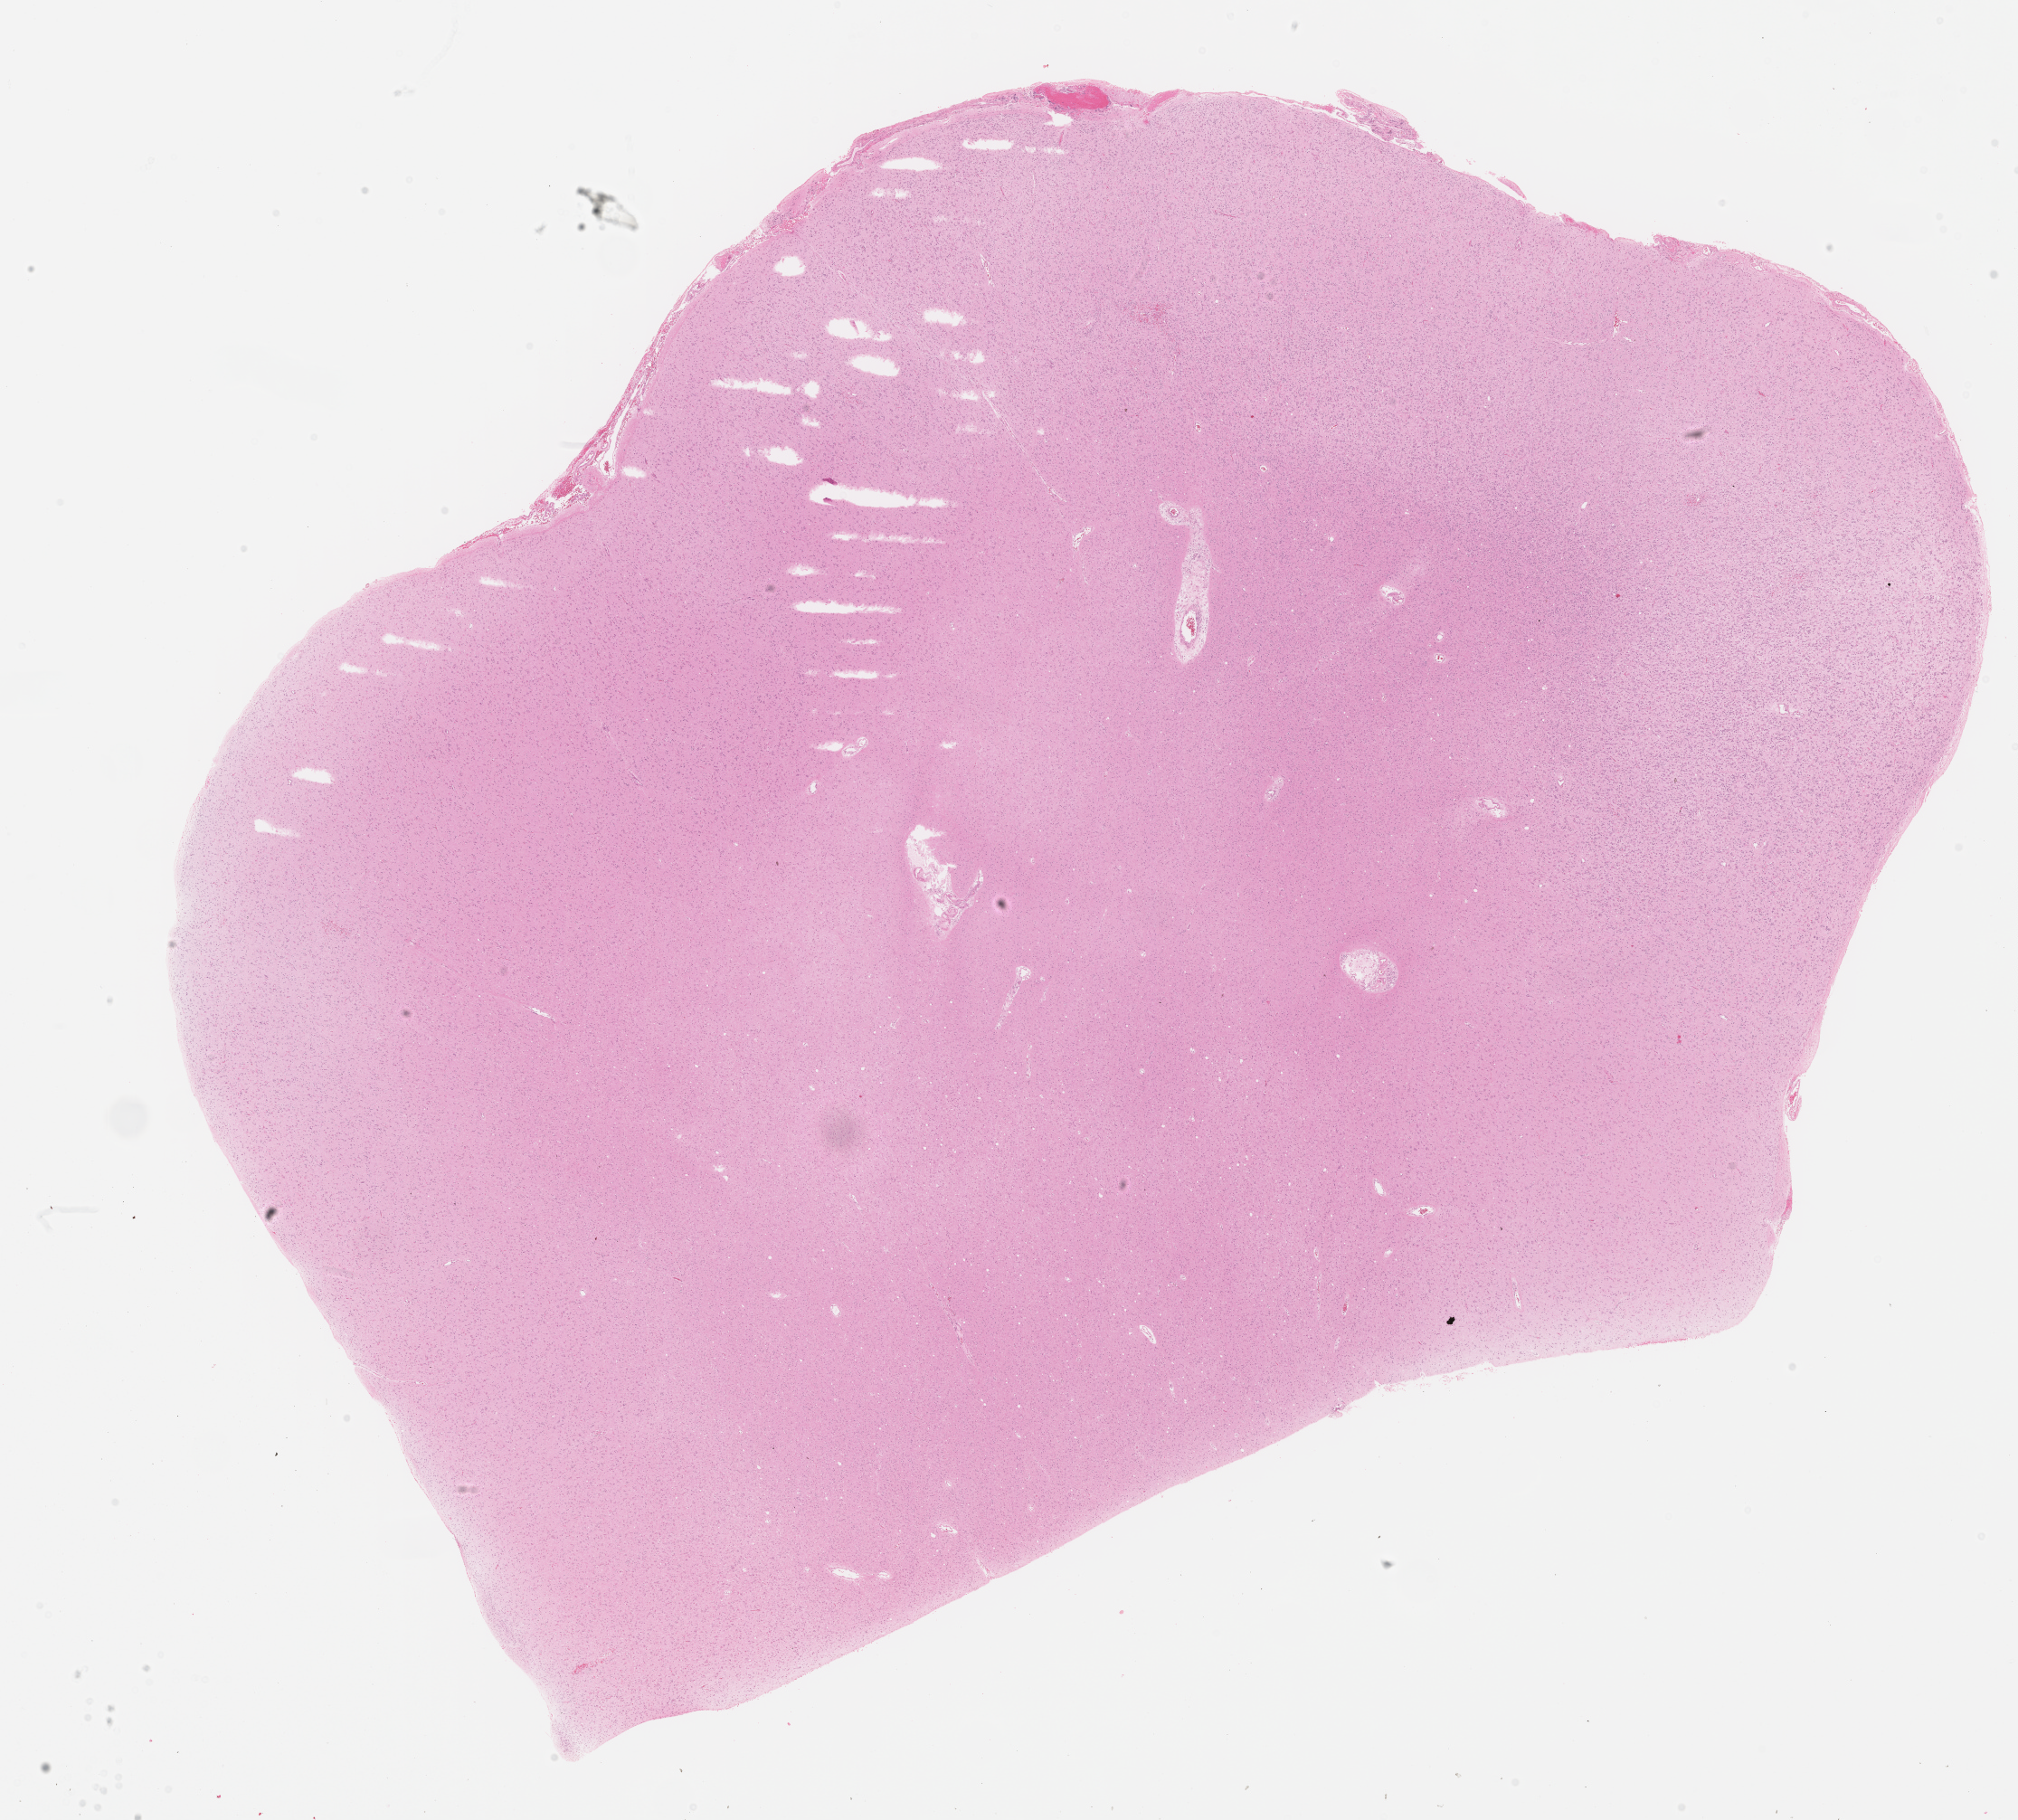
H&E whole-slide image, whole scanned area (about 18.0 x 16.2 mm, acquisition: 40x scan) shown as a low-resolution overview. Formalin-fixed paraffin-embedded (FFPE) diagnostic section. Sample: primary tumour, brain. Patient: male, age at initial diagnosis 40 years. Histologic grade: G2 (moderately differentiated).
* diagnosis: Oligodendroglioma, NOS (cerebrum)
* laterality: right